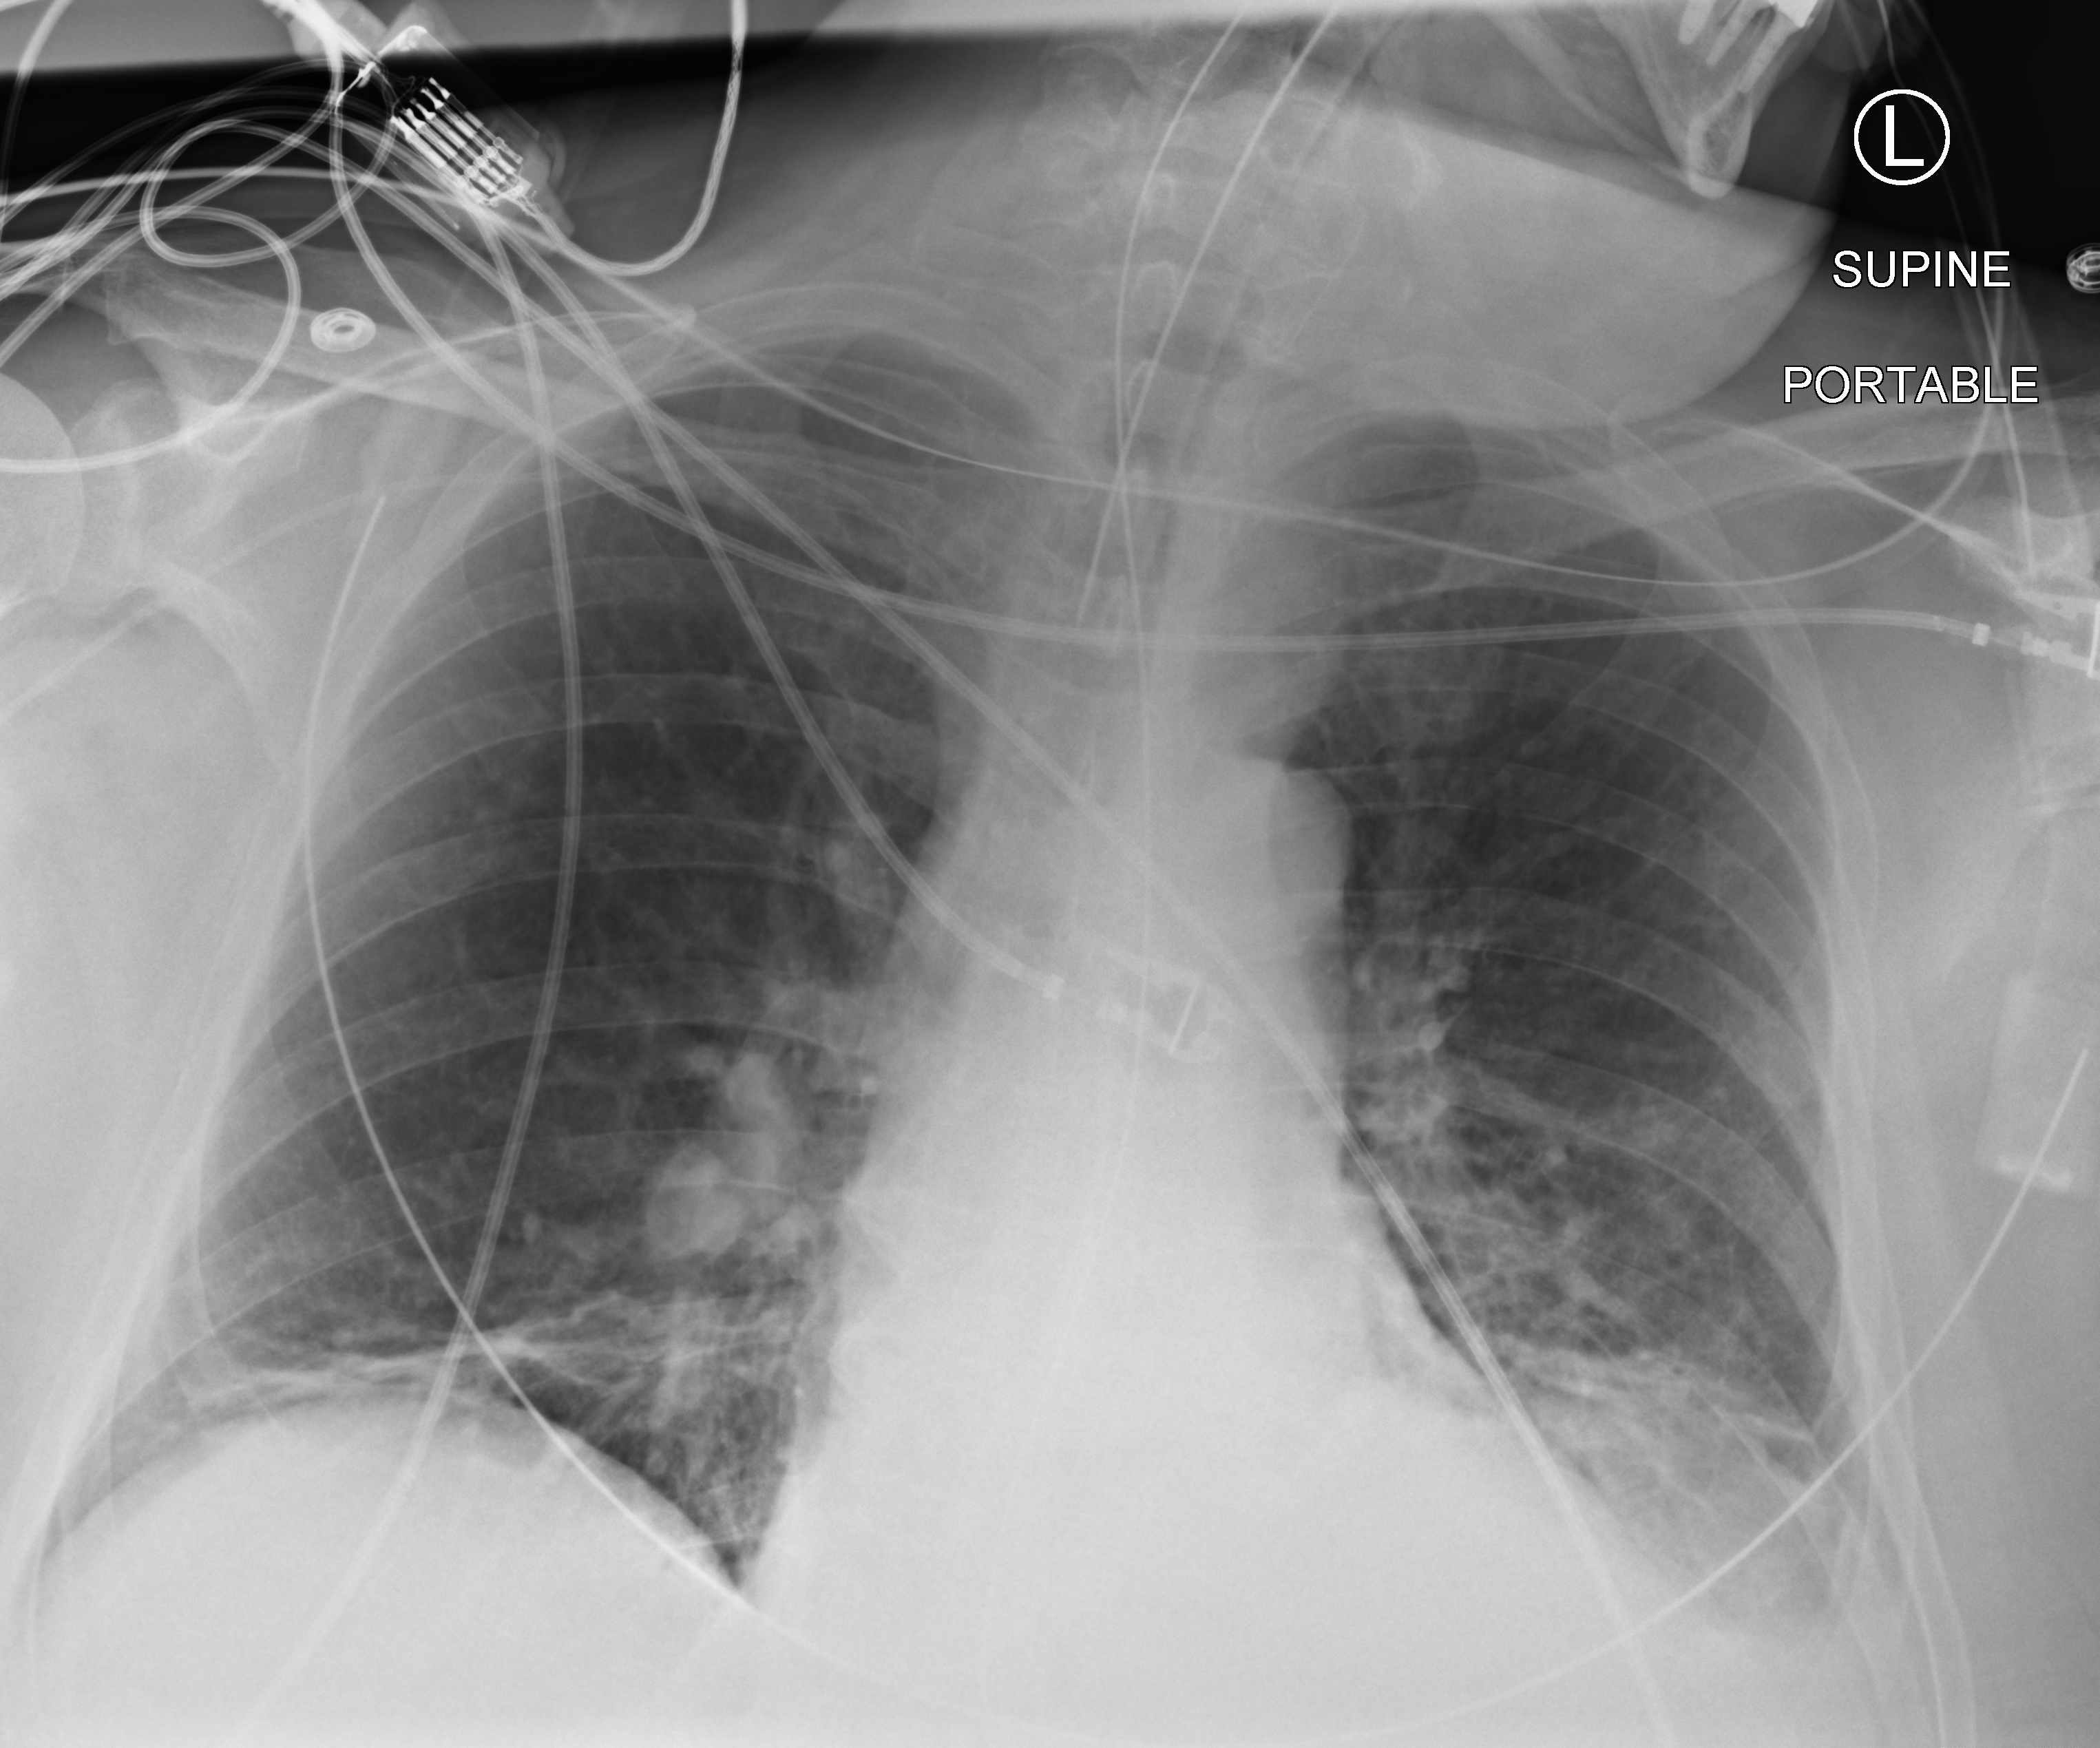
Portable chest radiograph. Patient hospitalised with COVID-19; male, aged 60–74 years.
Hospital-stay facts (about this admission, not read from this image; timing relative to this image not recorded): mechanically ventilated during this hospital stay: yes.